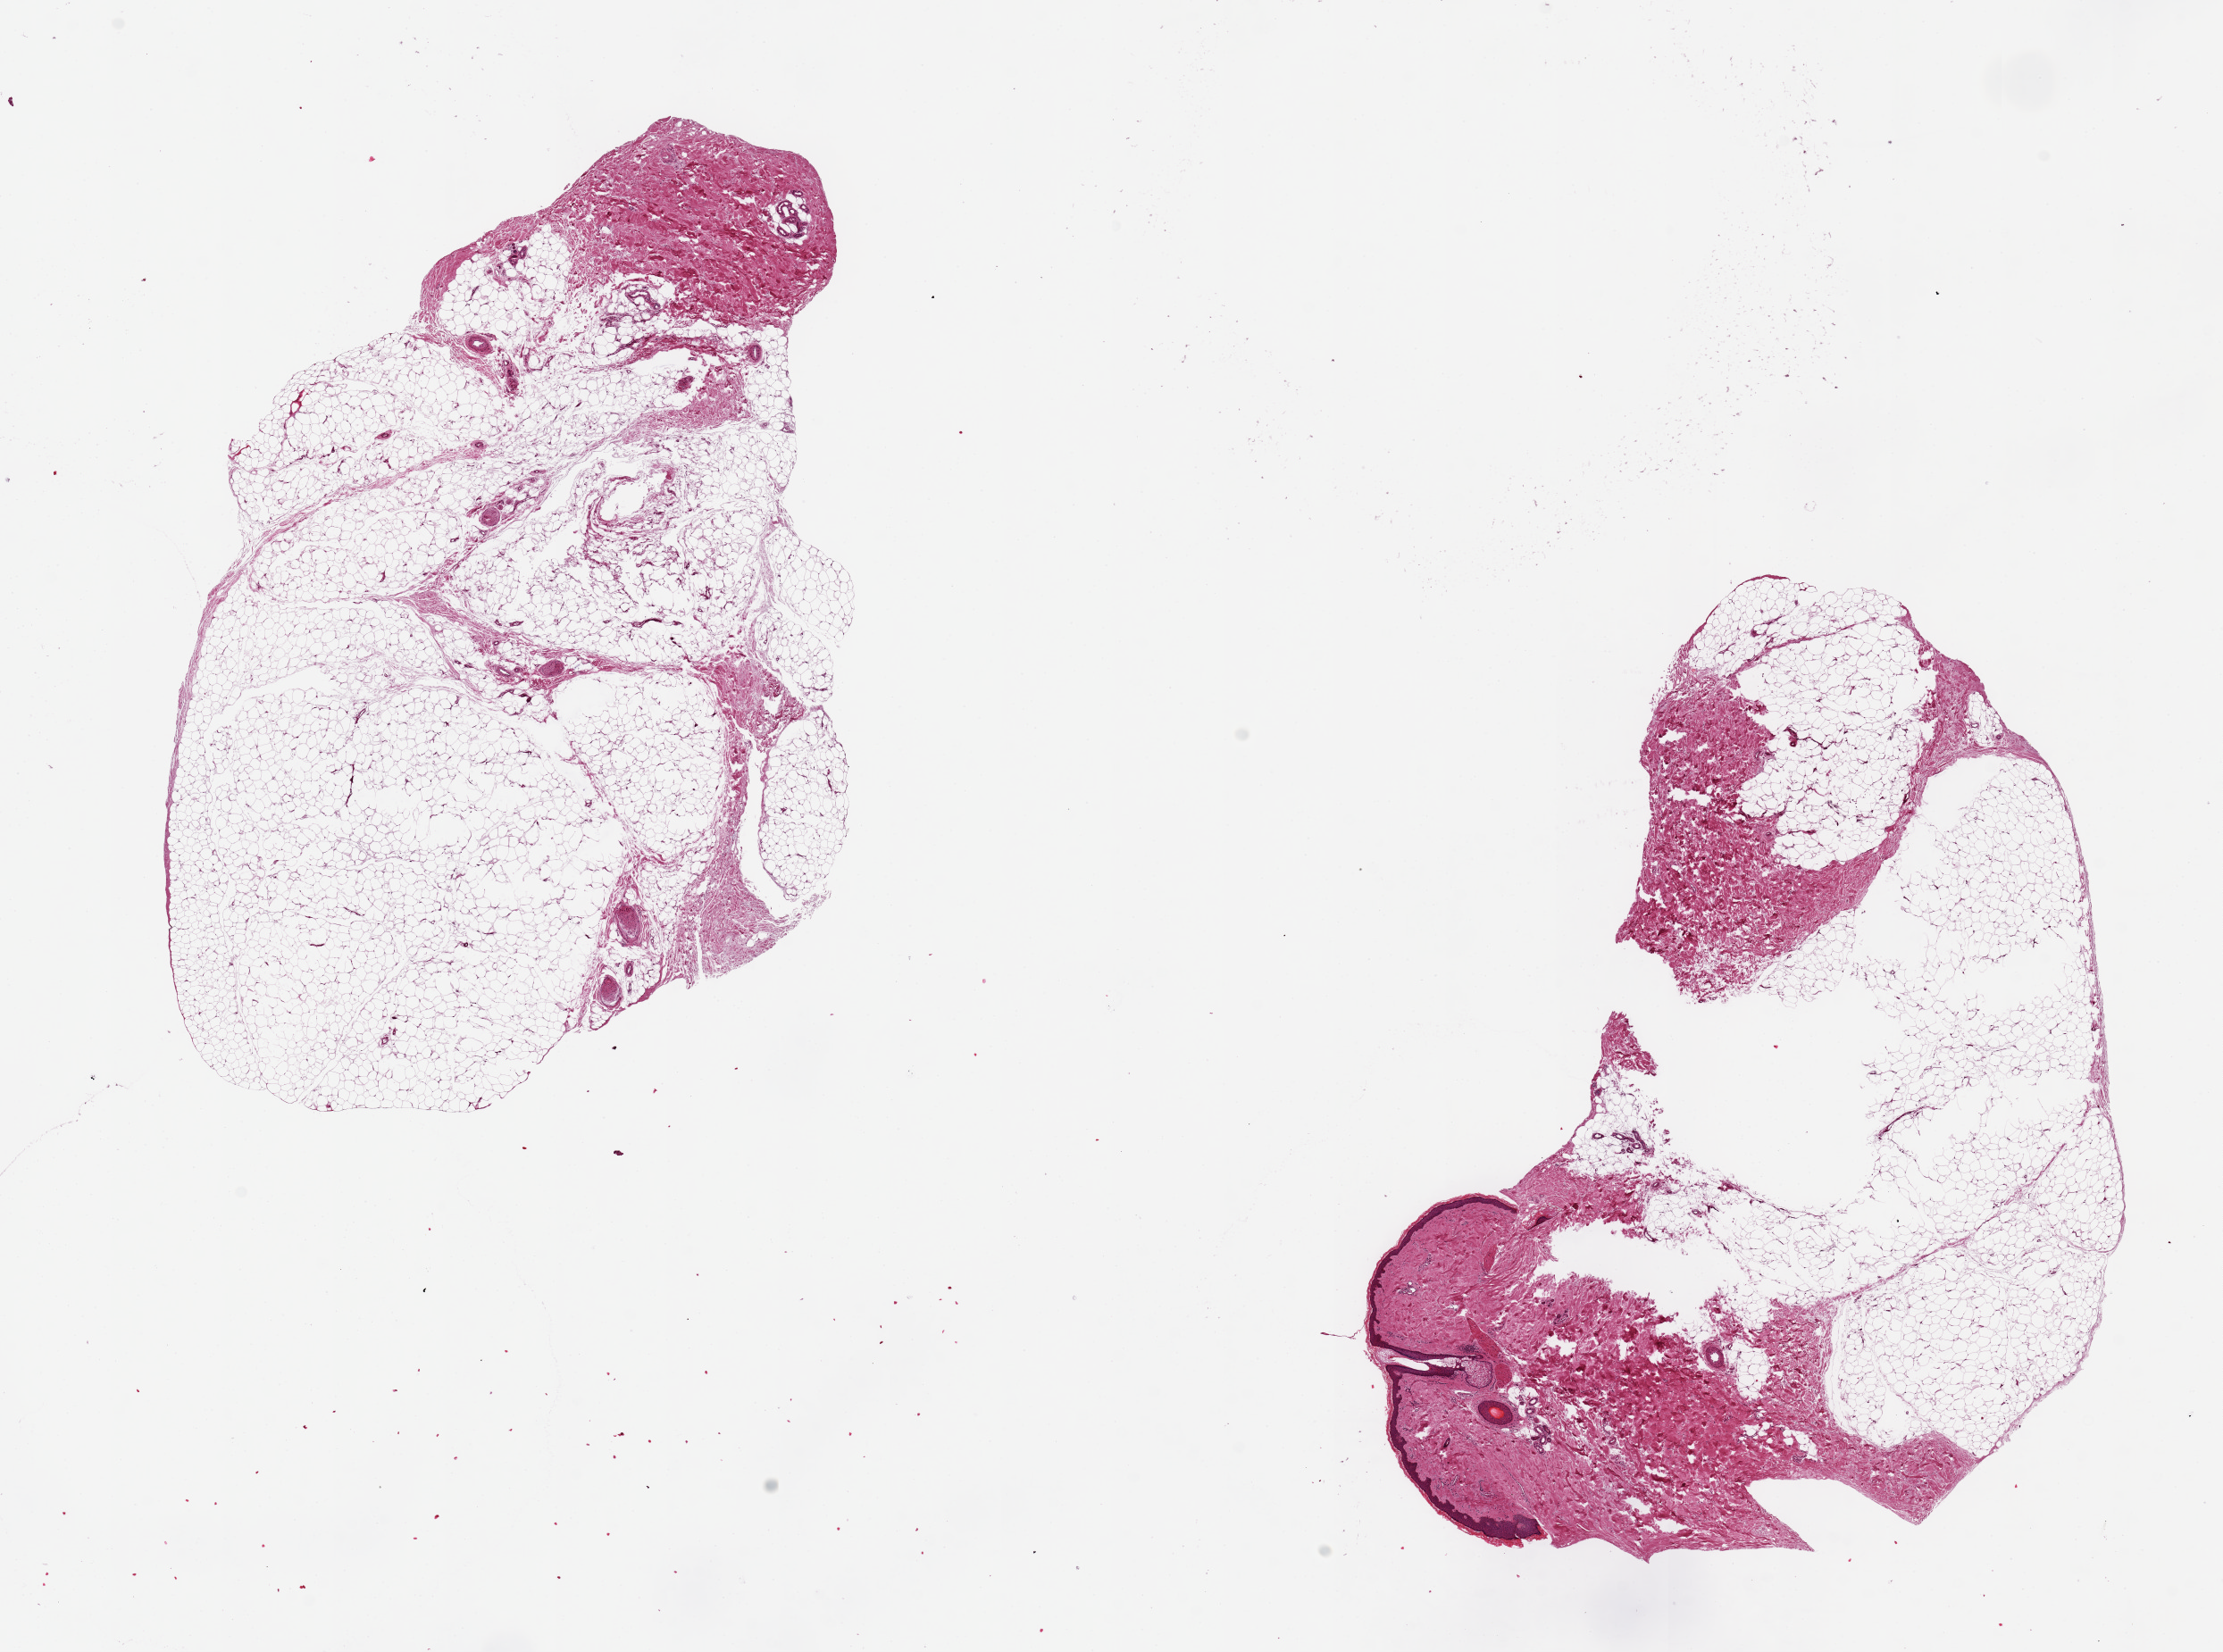
Haematoxylin and eosin whole-slide image — low-resolution overview of the scanned area, about 19.7 x 14.6 mm (from a 20x scan); PAXgene-fixed, paraffin-embedded tissue; sampled site (target tissue): adipose tissue; tissue donor sample. Donor: male.
Reviewer comment on this tissue sample: 2 pieces, ~8x5mm, NOTE: one with adherent skin.